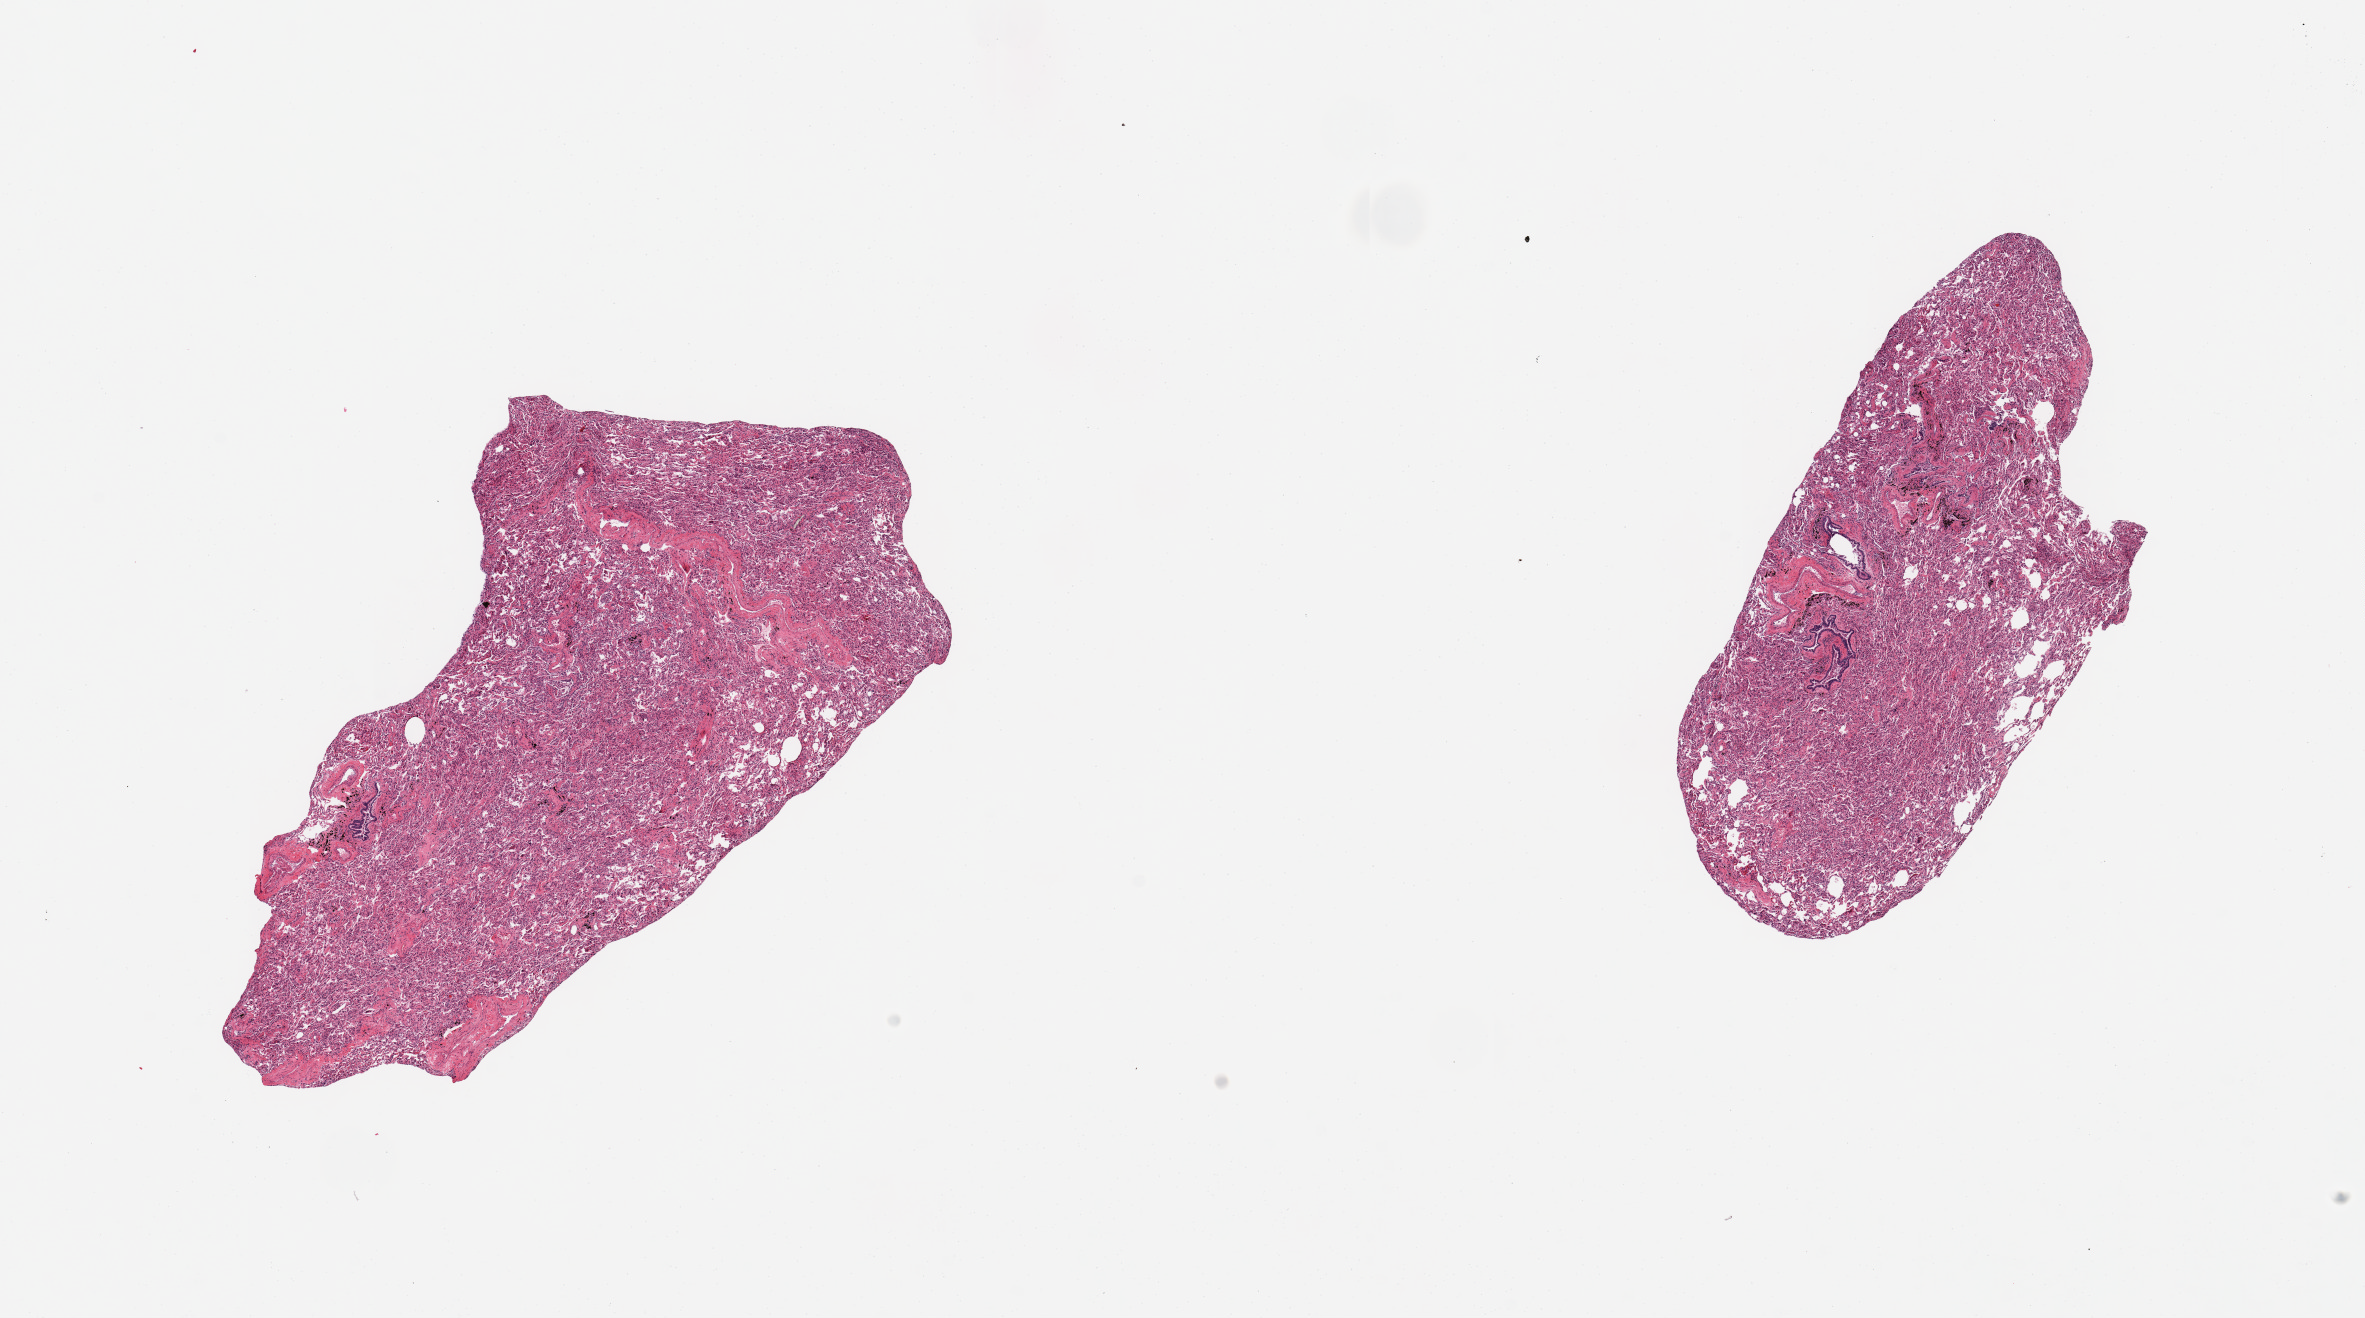
Hematoxylin and eosin (H&E) whole-slide image — low-resolution overview of the scanned area, about 18.7 x 10.4 mm; PAXgene-fixed, paraffin-embedded tissue; sampled site (target tissue): lung; donor tissue sample. Male donor.
Reviewer comment on this tissue sample: 2 pieces; atelectasis, focus of mild acute inflammatory cell infiltrate.